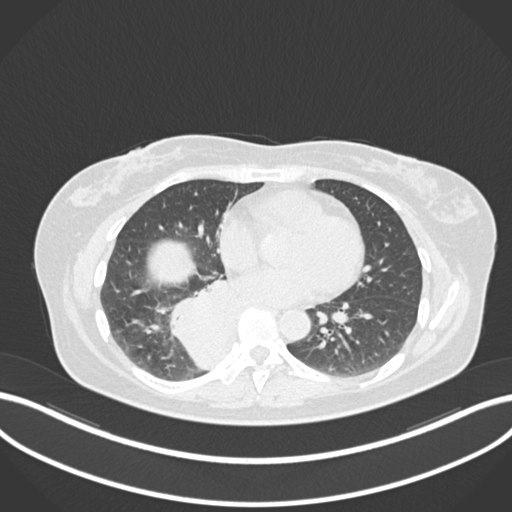
Chest CT, one axial slice; position 568 of 677 along the scan axis; reconstruction kernel B30f; 120 kVp; lung window (W 1500 / L -600 HU); 1 mm slice thickness; 512 × 512 image matrix, field of view 400 × 400 mm. Female patient, age 54 years. From the clinical record (not read from this slice): clinical TNM (as recorded): T4 N0 M0.
Annotated regions visible in this slice (rectangle marked by the reading radiologist):
- lung tumour (recorded histology: adenocarcinoma): box from (x=161, y=265) to (x=235, y=369) px